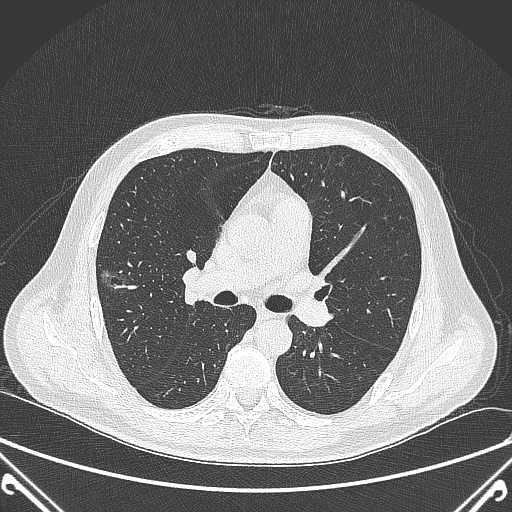
Chest CT, one axial slice. Slice 221 of 360 in the series (ordered by position). Lung window (W 1500 / L -600 HU). 1 mm slice thickness. 512 × 512 image matrix, field of view 380 × 380 mm. Patient: male, 64 years. Case-level facts recorded for this patient, not image findings: clinical TNM (as recorded): T1c N0 M0; histopathological grade: G2.
Annotated regions visible in this slice (rectangle marked by the reading radiologist):
- lung tumour (recorded histology: adenocarcinoma): bounding box <97,262,136,302> (left, top, right, bottom; pixels)